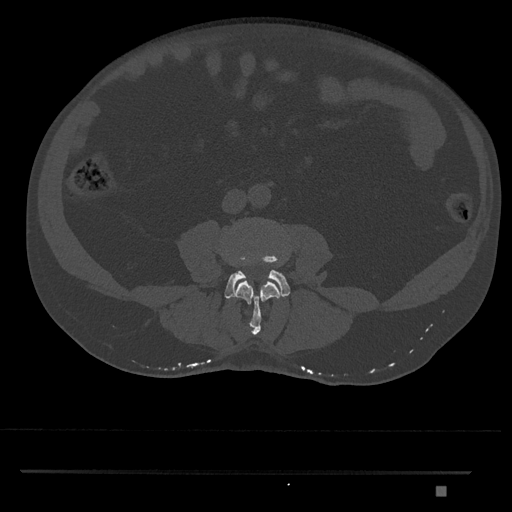
CT including the spine, one axial slice; slice 649 of 1134 in the series (ordered by position); reconstruction kernel Br40s/3; 120 kVp; bone window (W 1800 / L 400 HU); 0.5 mm slice thickness; 512 × 512 image matrix, field of view 429 × 429 mm. Male patient, age 65 years. Case-level facts recorded for this patient, not image findings: primary cancer: prostate.
Annotated regions visible in this slice (semi-automatic segmentation, software-assisted and operator-edited):
- L3 vertebra: bounding box [x1, y1, x2, y2] px = [235, 281, 280, 336]
- L4 vertebra: [224, 250, 290, 299]